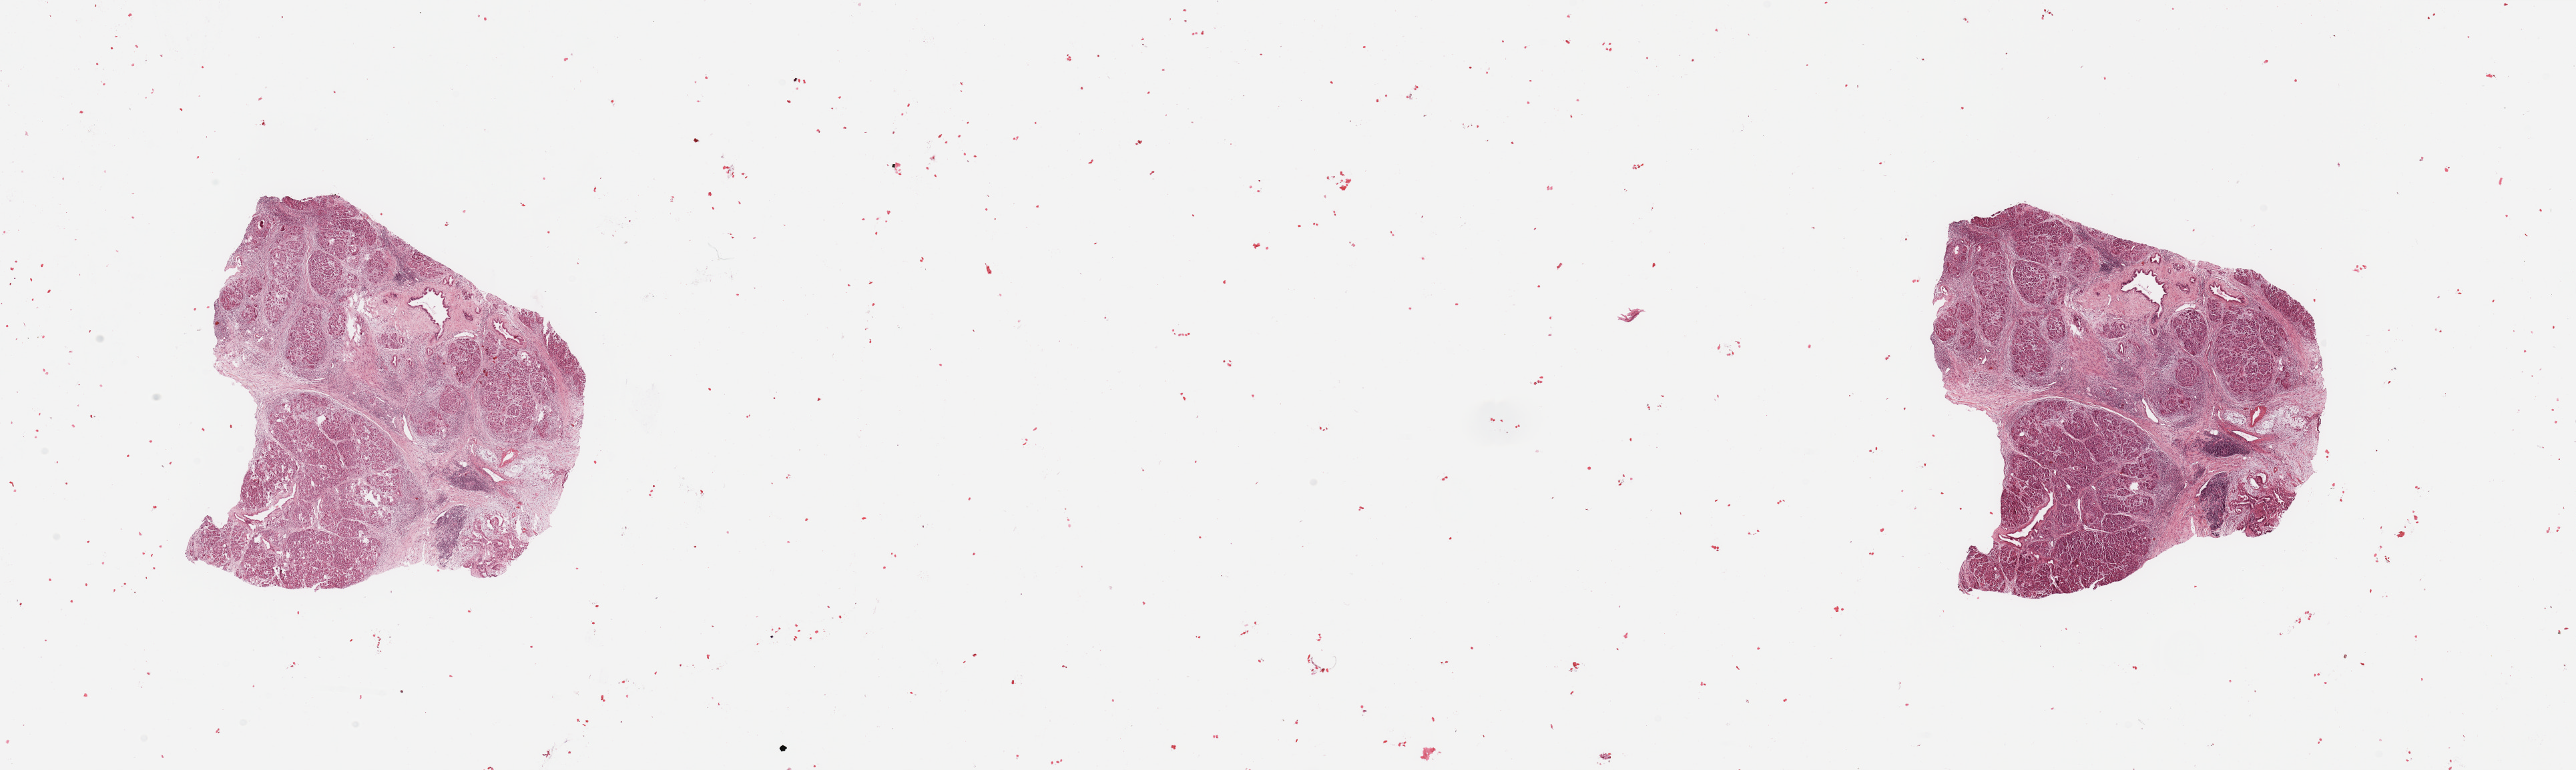
Digitized Hematoxylin and eosin (H&E) stained tissue section (whole slide), shown as a low-resolution overview of the whole scanned area (about 30.5 x 9.1 mm, from a 20x scan). Pancreas, normal (non-tumour) tissue. Patient: female, age 45 years.
• this section: normal (non-tumour) tissue from the same patient
• patient diagnosis: Infiltrating duct carcinoma, NOS